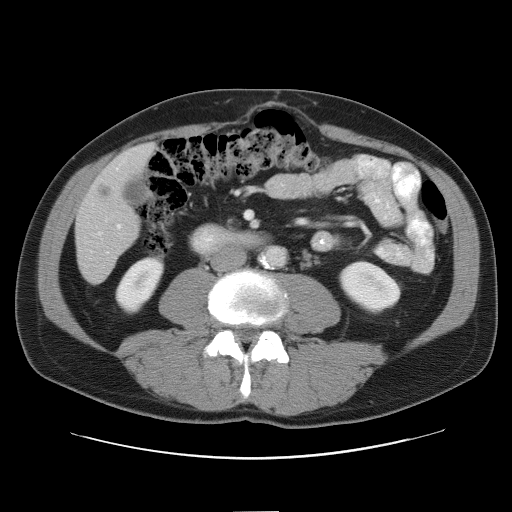
Contrast-enhanced abdominal CT, one axial slice; slice 17 of 52 in the series (ordered by position); 120 kVp; intravenous contrast given; soft-tissue window (W 400 / L 40 HU); 5 mm slice thickness; 512 × 512 image matrix, field of view 393 × 393 mm. Male patient, age 70 years. From the clinical record (not read from this slice): diagnosis: colorectal cancer liver metastases, imaged before liver resection; multiple liver metastases: yes; largest metastasis: 4 cm.
Outlined on this slice (outlined manually by an expert reader):
- hepatic veins: bounding box <98,232,101,235> (left, top, right, bottom; pixels)
- liver: <76,145,153,283>
- planned liver remnant (the part of the liver to remain after resection): <121,145,153,174>
- portal vein (with intrahepatic branches): <117,224,122,229>
- liver metastasis: <98,186,111,200>